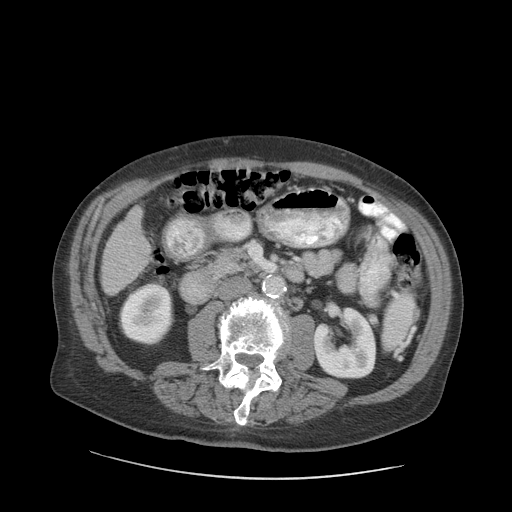
Contrast-enhanced abdominal CT (liver protocol), one axial slice; reconstruction kernel STANDARD; 140 kVp; soft-tissue window (W 400 / L 40 HU); 2.5 mm slice thickness; 512 × 512 image matrix, field of view 420 × 420 mm. Case-level facts recorded for this patient, not image findings: diagnosis: hepatocellular carcinoma (patient treated with transarterial chemoembolisation; whether this scan precedes or follows treatment is not stated here); TNM stage (as recorded): Stage-I; Child-Pugh class: A; tumour differentiation: moderately differentiated.
Annotated regions visible in this slice (semi-automatic segmentation, software-assisted and operator-edited):
- liver parenchyma outside the tumour (the mass and vessels are separate outlines, so this box may not span the whole liver): bounding box (x1, y1, x2, y2) in pixels: (100, 206, 150, 294)